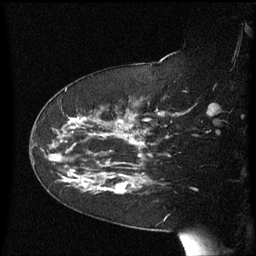
Breast MRI (dynamic contrast-enhanced), one sagittal slice. Slice 39 of 60 in the series (ordered by position). Dynamic contrast-enhanced series, image 2 of 3 at this slice position (ordered by acquisition). 1.5 T. TE 4.2 ms, TR 8.4 ms. 2.3 mm slice thickness. 256 × 256 image matrix, field of view 200 × 200 mm. Patient: female, 63 years. From the clinical record (not read from this slice): setting: breast cancer imaged before/during neoadjuvant chemotherapy; receptor status: HER2-positive.
Structures marked on this image (semi-automatic segmentation, software-assisted and operator-edited):
- analysis volume of interest (the breast-tissue region the enhancement analysis was run in; not a lesion): bounding box [x1, y1, x2, y2] px = [63, 144, 147, 205]
- tumour enhancement mask (voxels above the 70 % enhancement threshold inside the analysis volume of interest): [63, 144, 143, 194]